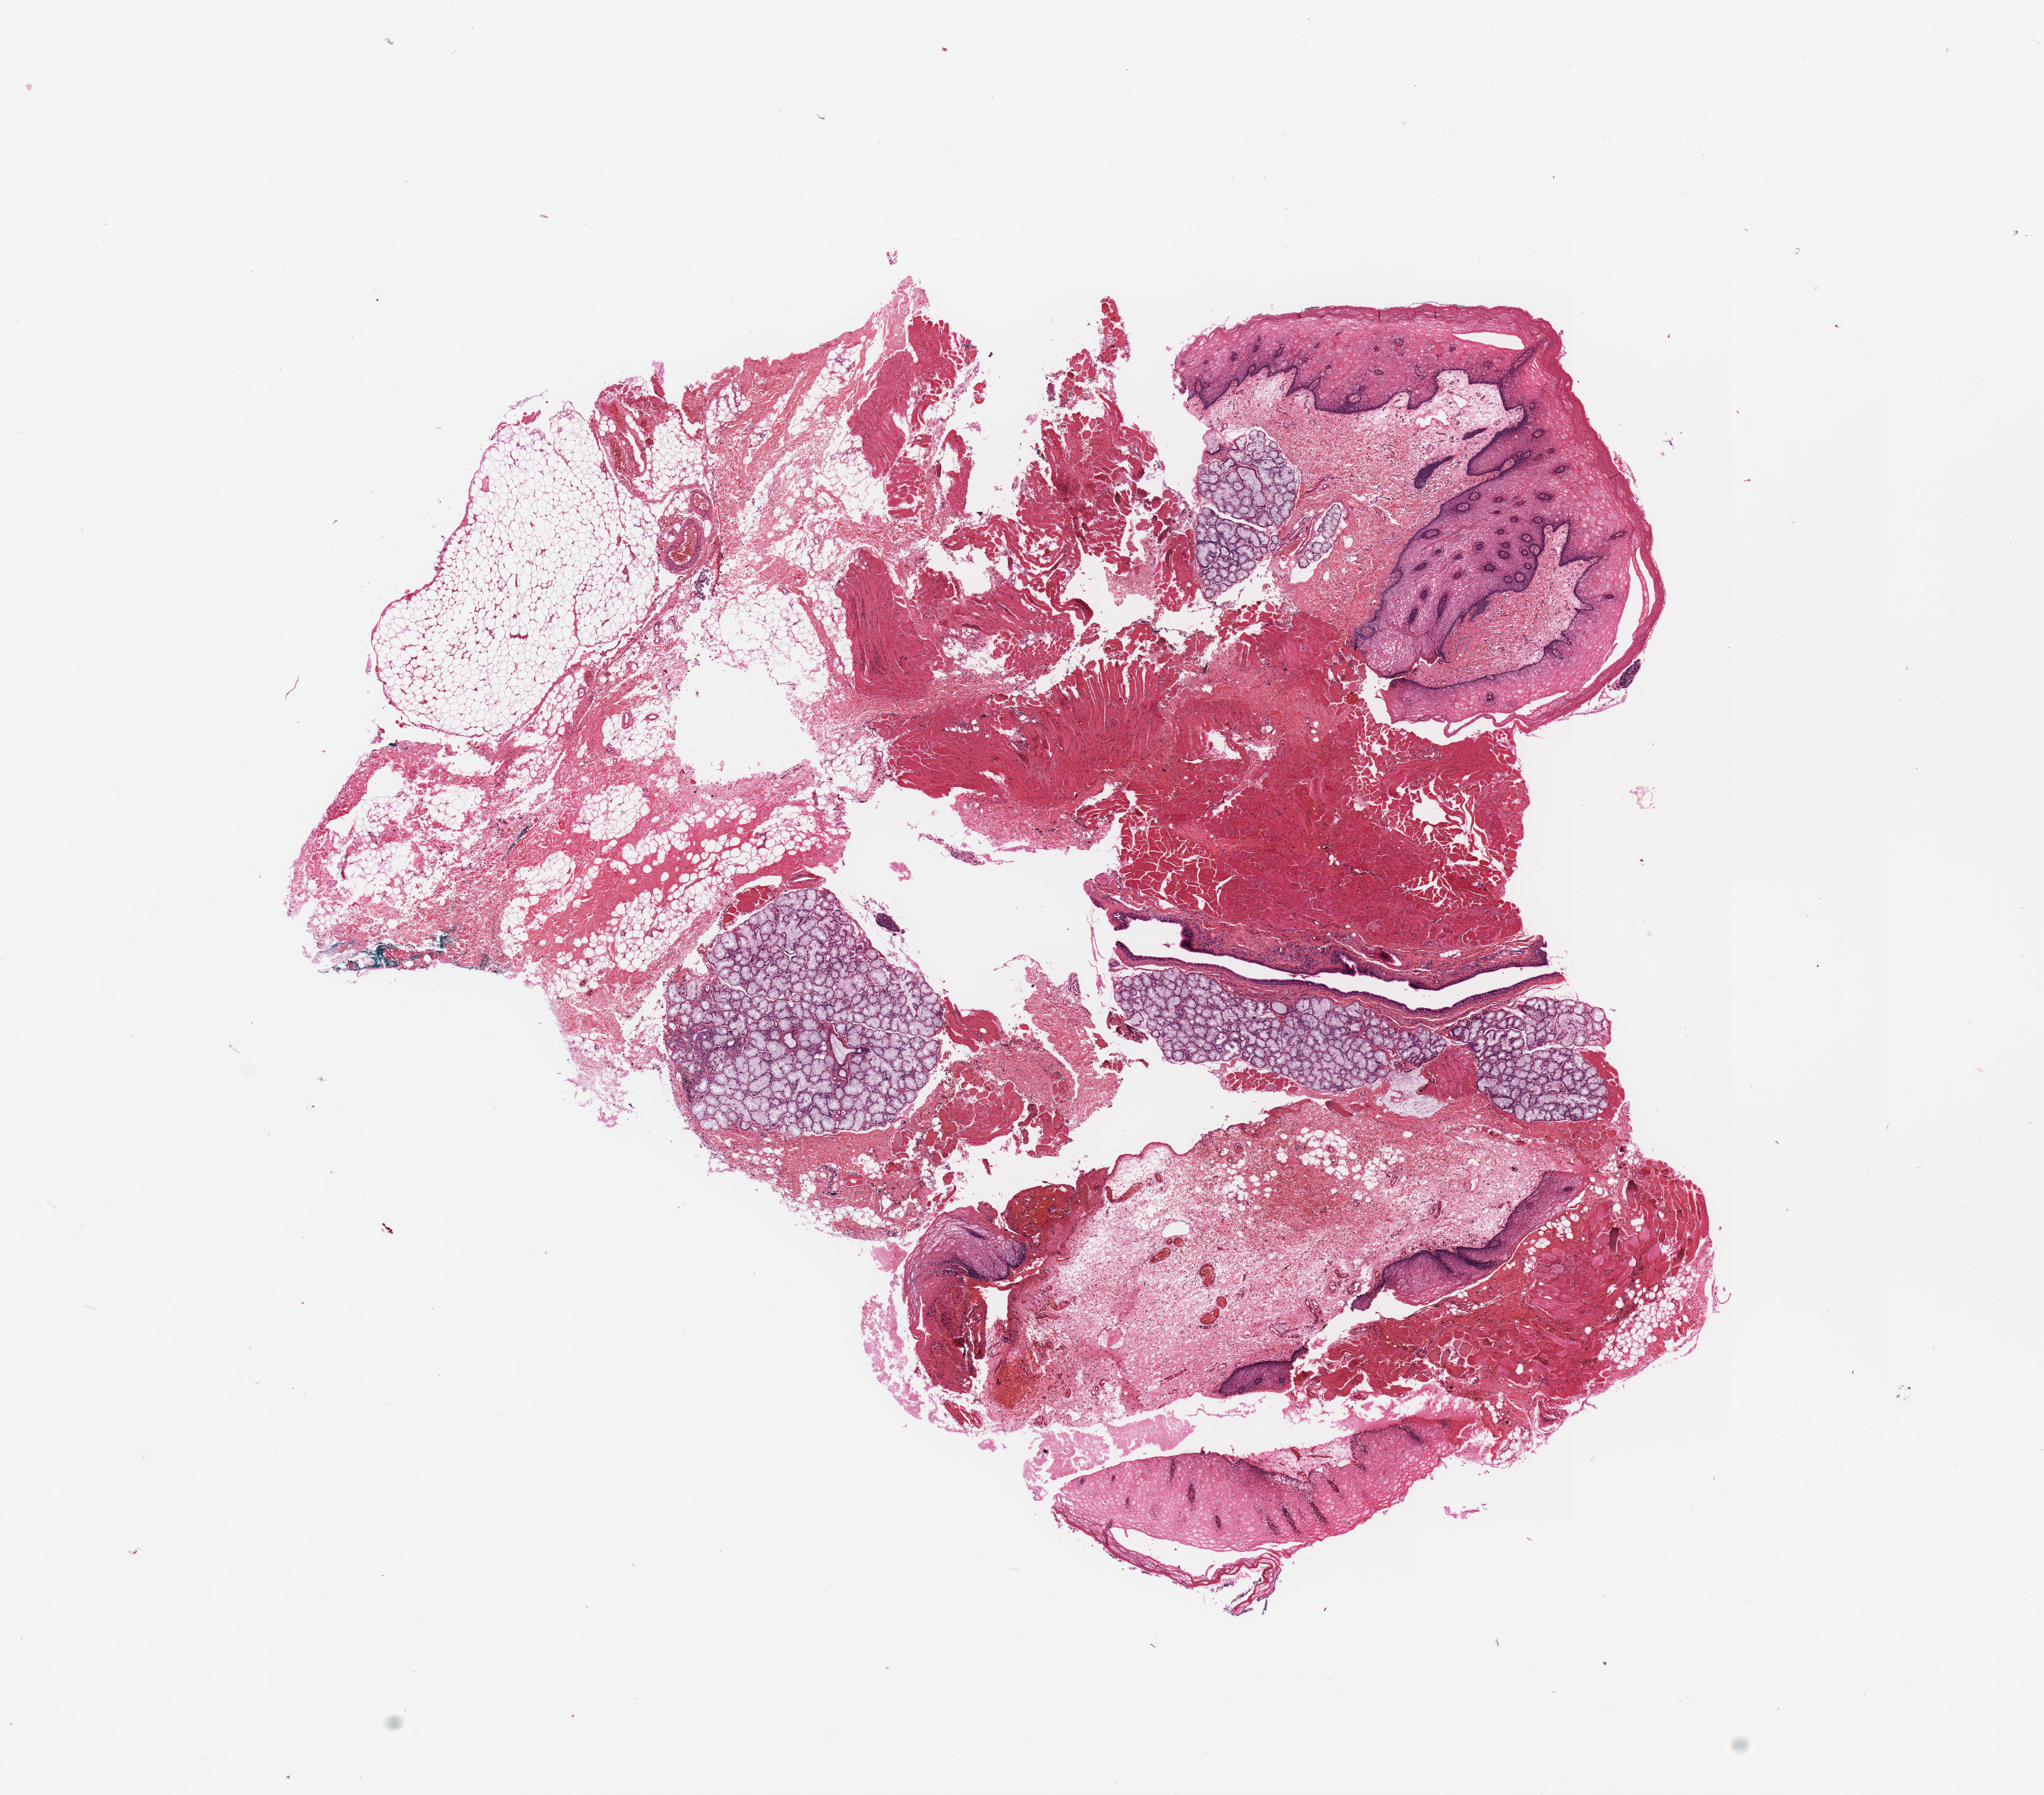
Hematoxylin and eosin (H&E) stained whole-slide image, low-resolution overview of the scanned area, about 12.8 x 11.2 mm. Normal (non-tumour) tissue sample, sampled site: oropharynx. 47-year-old male patient.
• this section: normal (non-tumour) tissue from the same patient
• patient diagnosis: Squamous cell carcinoma, NOS (oropharynx, NOS)